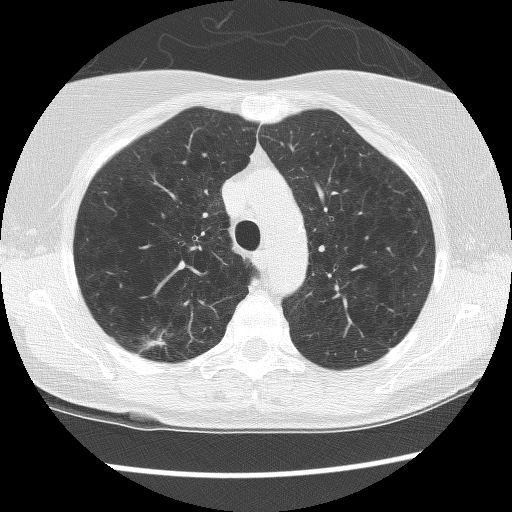
Low-dose screening chest CT, axial slice. Second screening round (one year after baseline). Lung window (W 1500 / L -600 HU). Slice 33 of 134 in the series. Female participant, aged 63 years at enrolment. Former smoker at enrolment.
Expert reader's lesion annotation, bounding box <128,320,191,366> (left, top, right, bottom; pixels). The exam's reader record, not a measurement of the box and not confirmed to be the same lesion: non-calcified nodule or mass ≥4 mm, right upper lobe, 16 × 7 mm, spiculated (stellate) margins, mixed attenuation, pre-existing on the prior screen: yes; interval growth: yes. Official screen result: positive, other. Participant outcome: lung cancer diagnosed 43 days after this screen — bronchiolo-alveolar carcinoma, non-mucinous, right upper lobe, well differentiated (G1), stage IA (AJCC 6th edition), 12 mm at pathology.